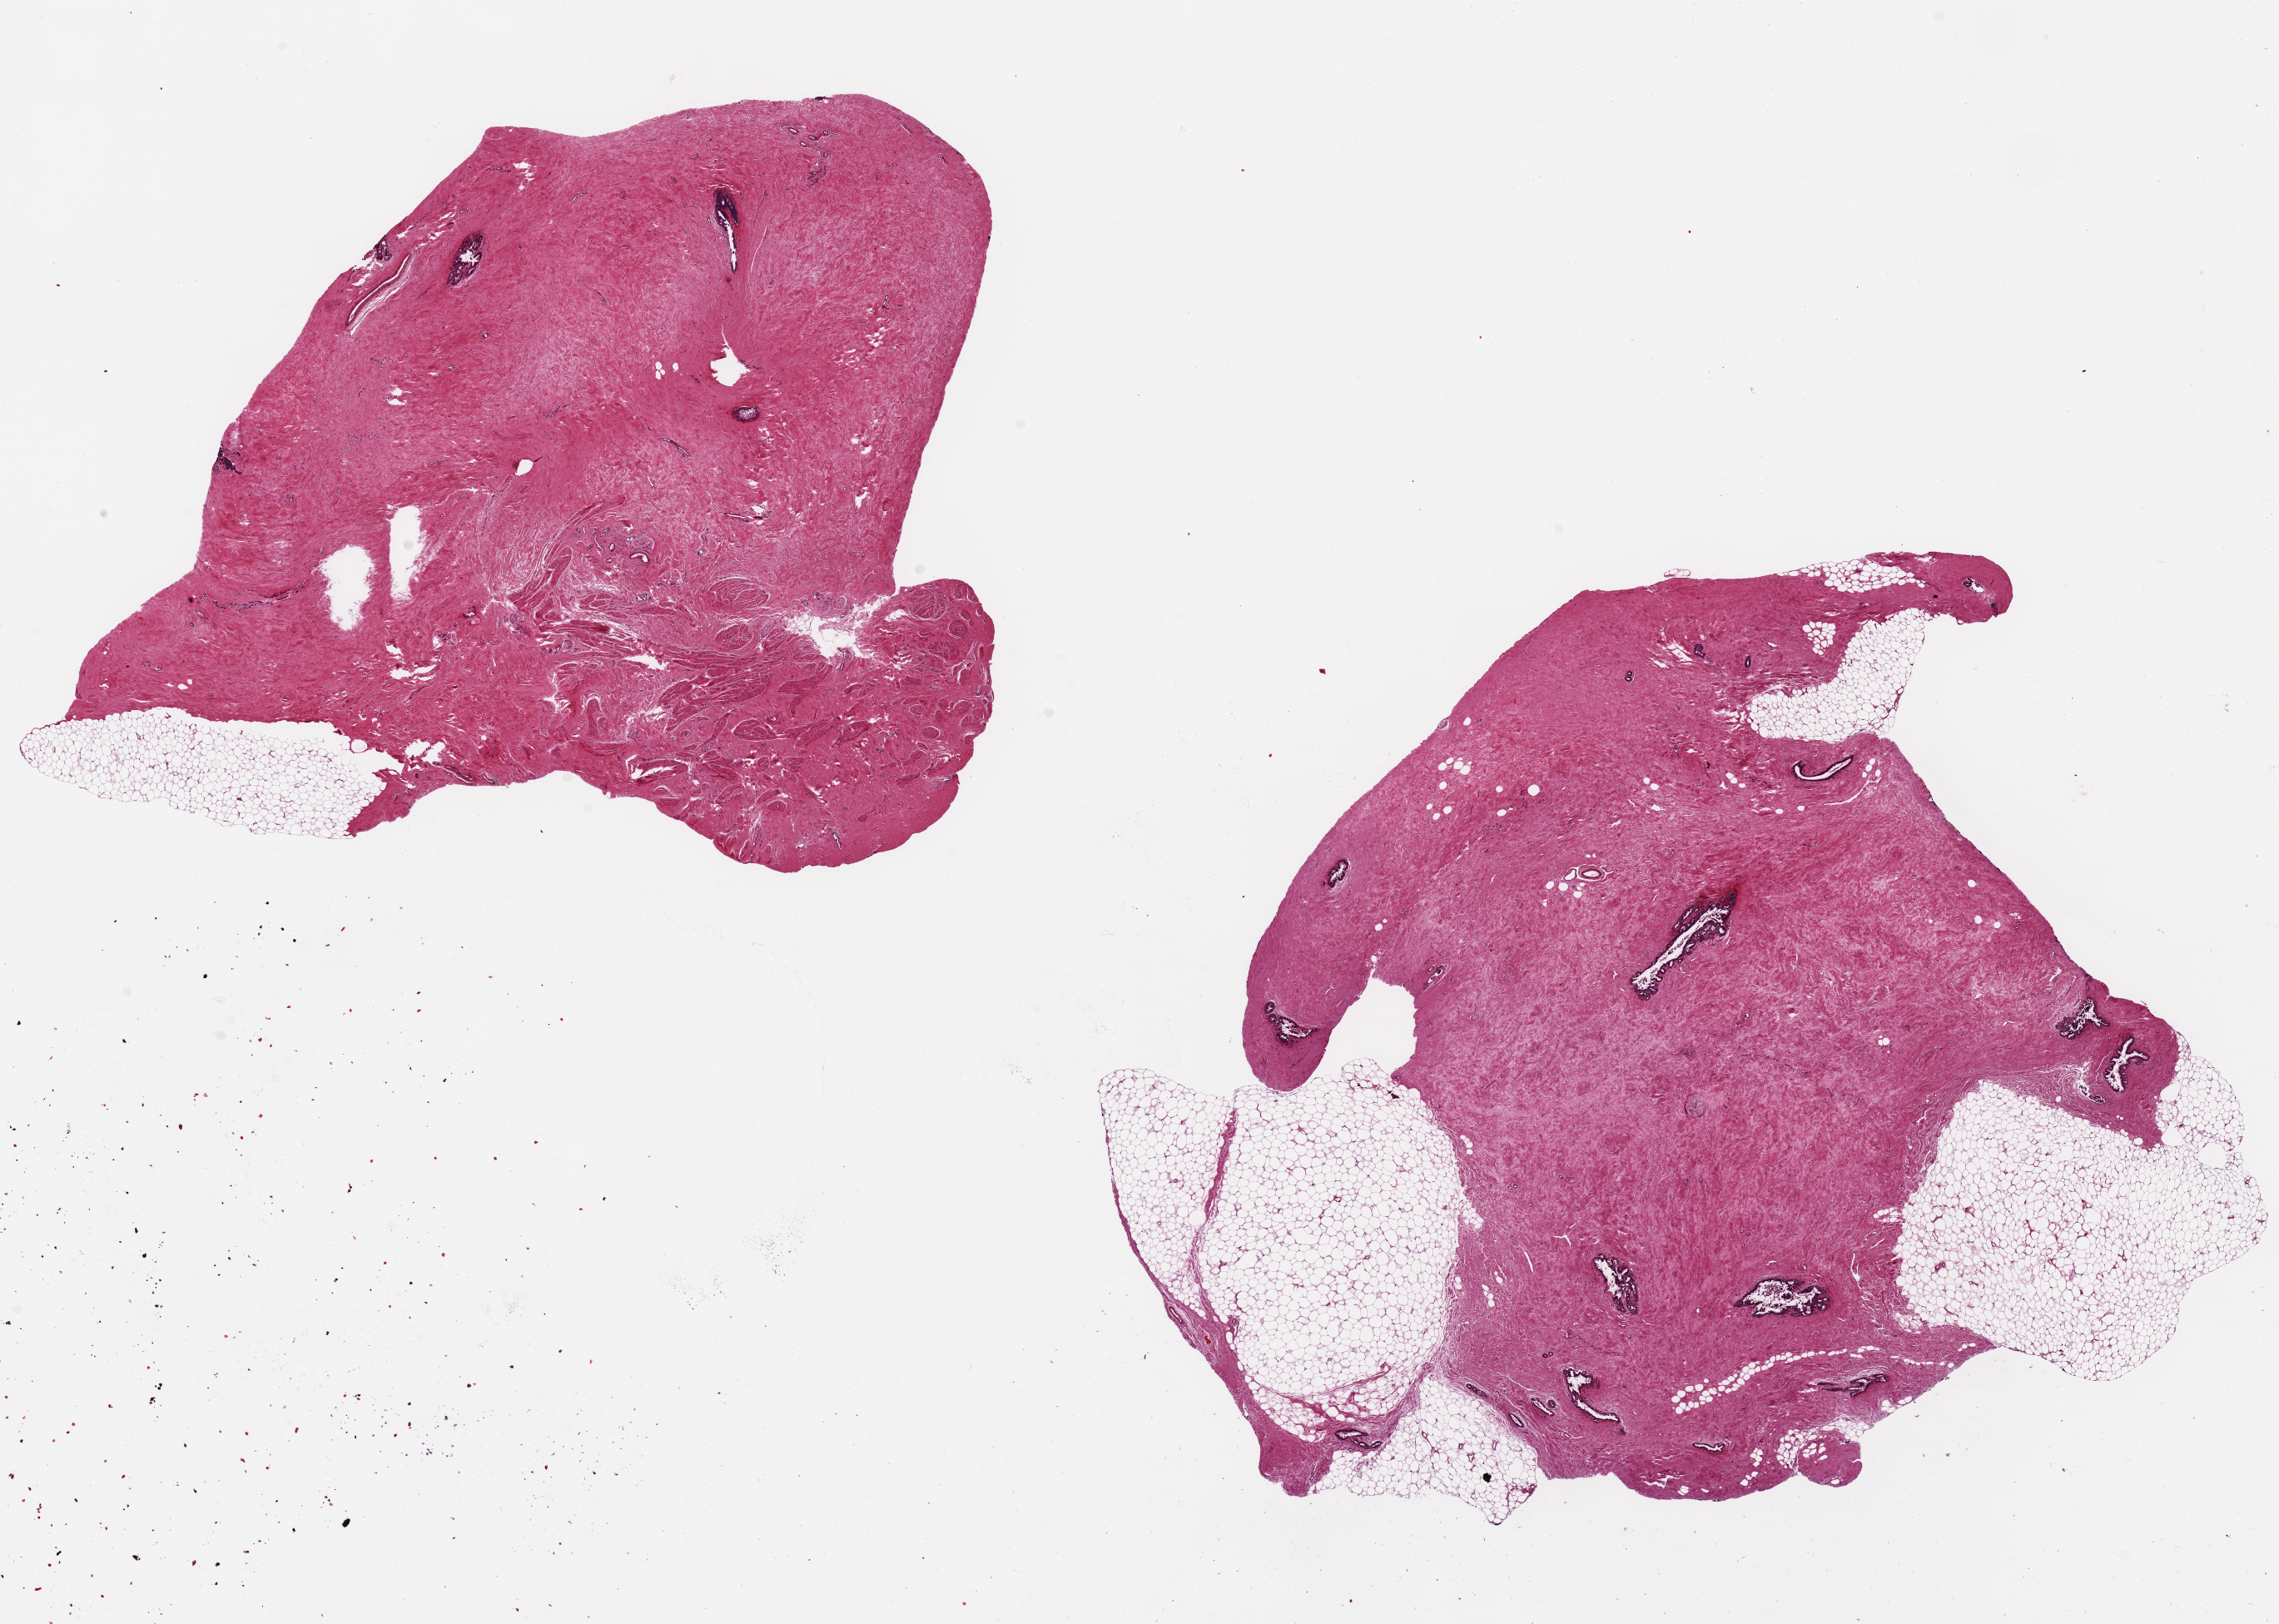
Whole-slide image, H&E stain, a low-resolution overview of the entire scanned area, about 21.7 x 15.4 mm (slide scanned at 20x). PAXgene-fixed, paraffin-embedded tissue. Sampled site (target tissue): breast. Tissue donor sample.
Reviewer comment on this tissue sample: 2 aliquots, ~9x8mm. Gynecomastoid hyperplasia in mammary ductal uniits, background gynecomastoid change.